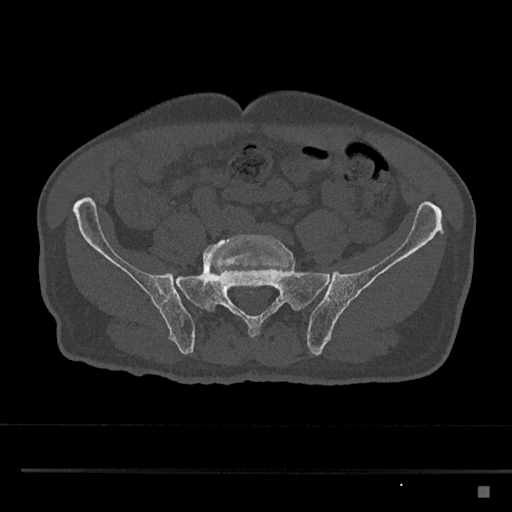
CT including the spine, one axial slice; slice 548 of 797 in the series (ordered by position); reconstruction kernel Br40s/3; bone window (W 1800 / L 400 HU); 0.5 mm slice thickness; 512 × 512 image matrix. Patient: male, 59 years. From the clinical record (not read from this slice): primary cancer: prostate.
Outlined on this slice (semi-automatically segmented with operator editing):
- L5 vertebra: bounding box [x1, y1, x2, y2] px = [203, 235, 292, 274]